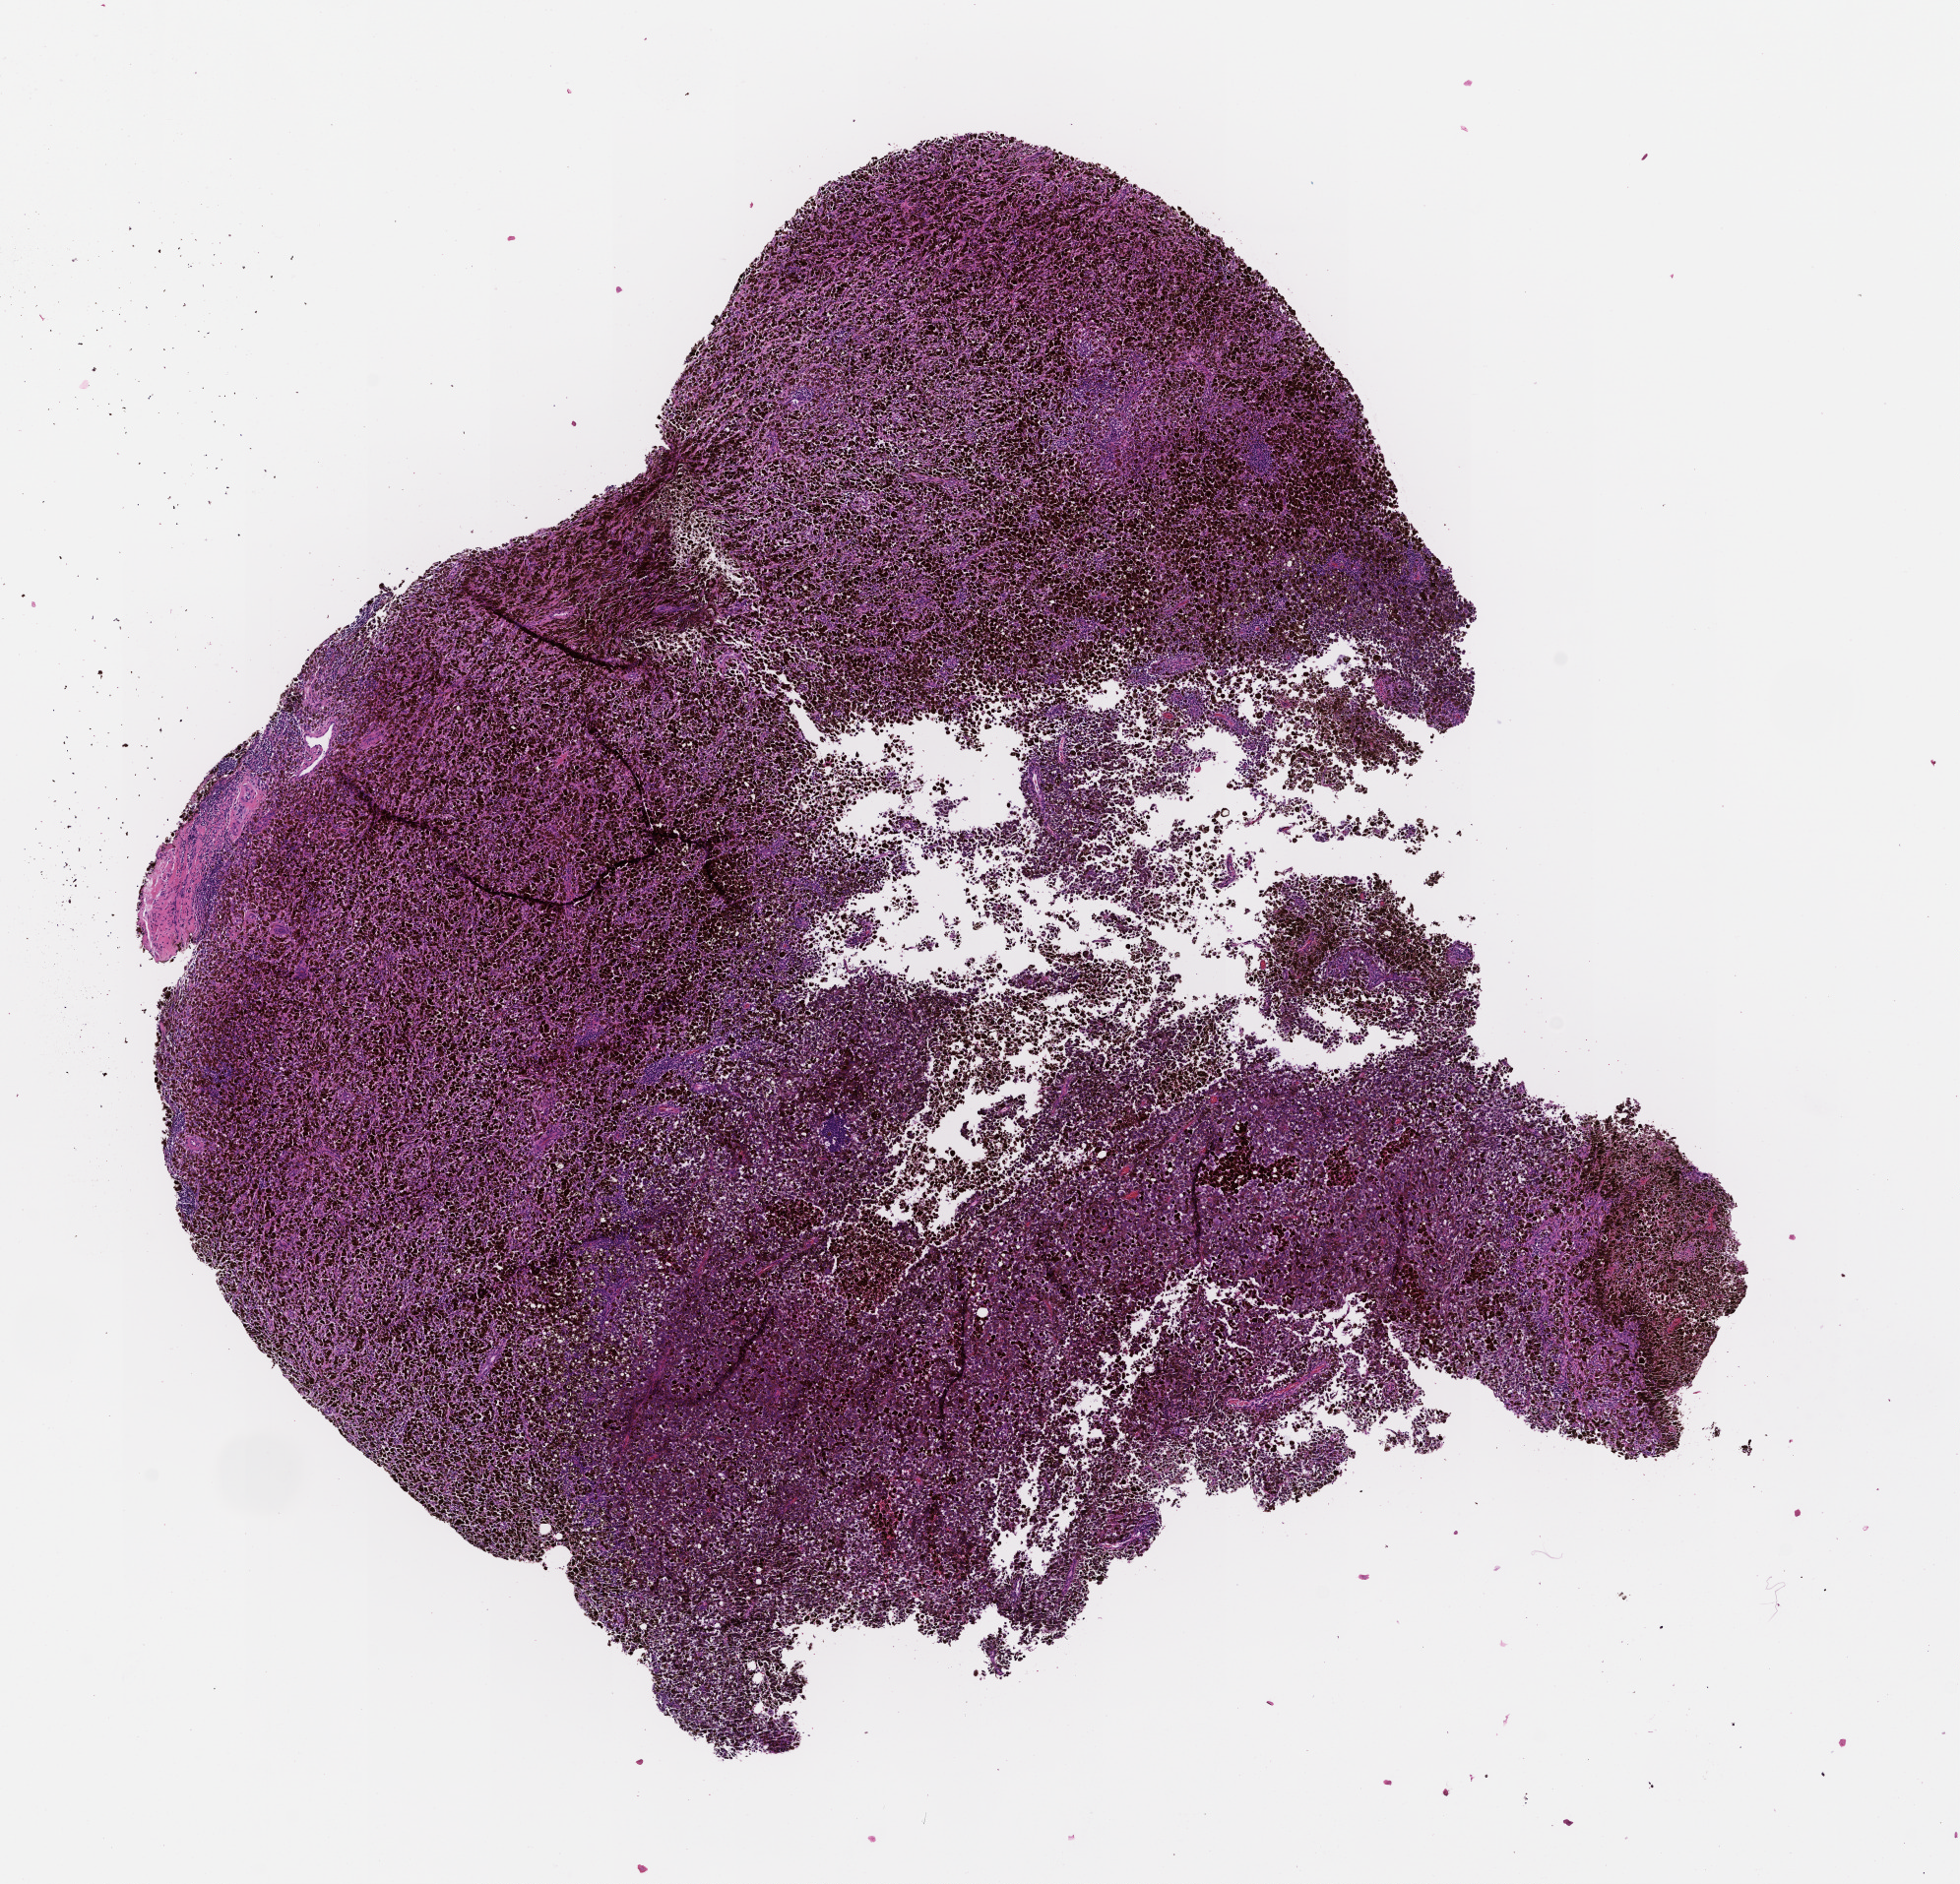
Digitized H&E-stained section, shown as a low-resolution overview of the whole scanned area (about 8.0 x 7.7 mm), formalin-fixed, paraffin-embedded (FFPE) tissue, collected at baseline (before treatment). Patient: male.
This section: metastatic tumor tissue. Patient diagnosis (primary): Melanoma.